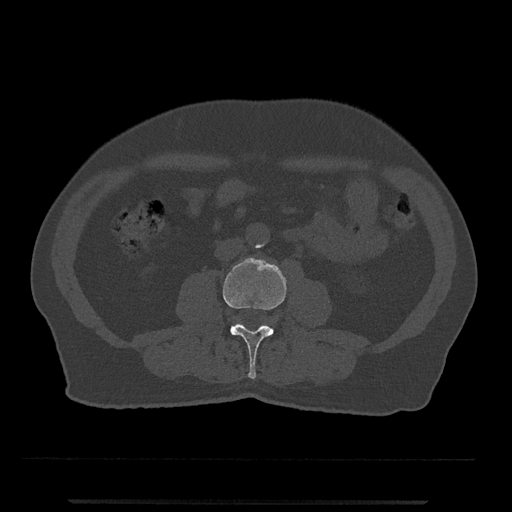
CT including the spine, one axial slice. 120 kVp. Bone window (W 1800 / L 400 HU). 0.5 mm slice thickness. 512 × 512 image matrix, field of view 419 × 419 mm. Male patient, age 63 years. Case-level facts recorded for this patient, not image findings: primary cancer: prostate.
Outlined on this slice (semi-automatic segmentation, software-assisted and operator-edited):
- L3 vertebra: bounding box <223,257,286,379> (left, top, right, bottom; pixels)